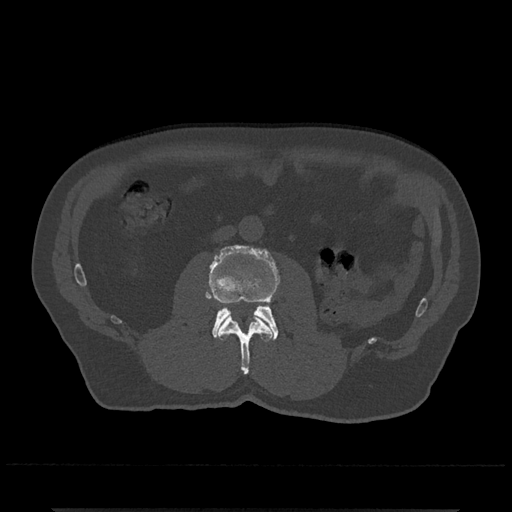
CT including the spine, one axial slice. Slice 254 of 797 in the series (ordered by position). Reconstruction kernel Br40s/3. 120 kVp. Bone window (W 1800 / L 400 HU). 512 × 512 image matrix, field of view 393 × 393 mm. Male patient, age 67 years. Case-level facts recorded for this patient, not image findings: primary cancer: prostate.
Structures marked on this image (semi-automatic segmentation, software-assisted and operator-edited):
- L2 vertebra: box from (x=217, y=314) to (x=273, y=375) px
- L3 vertebra: (x=206, y=245)–(x=280, y=341)